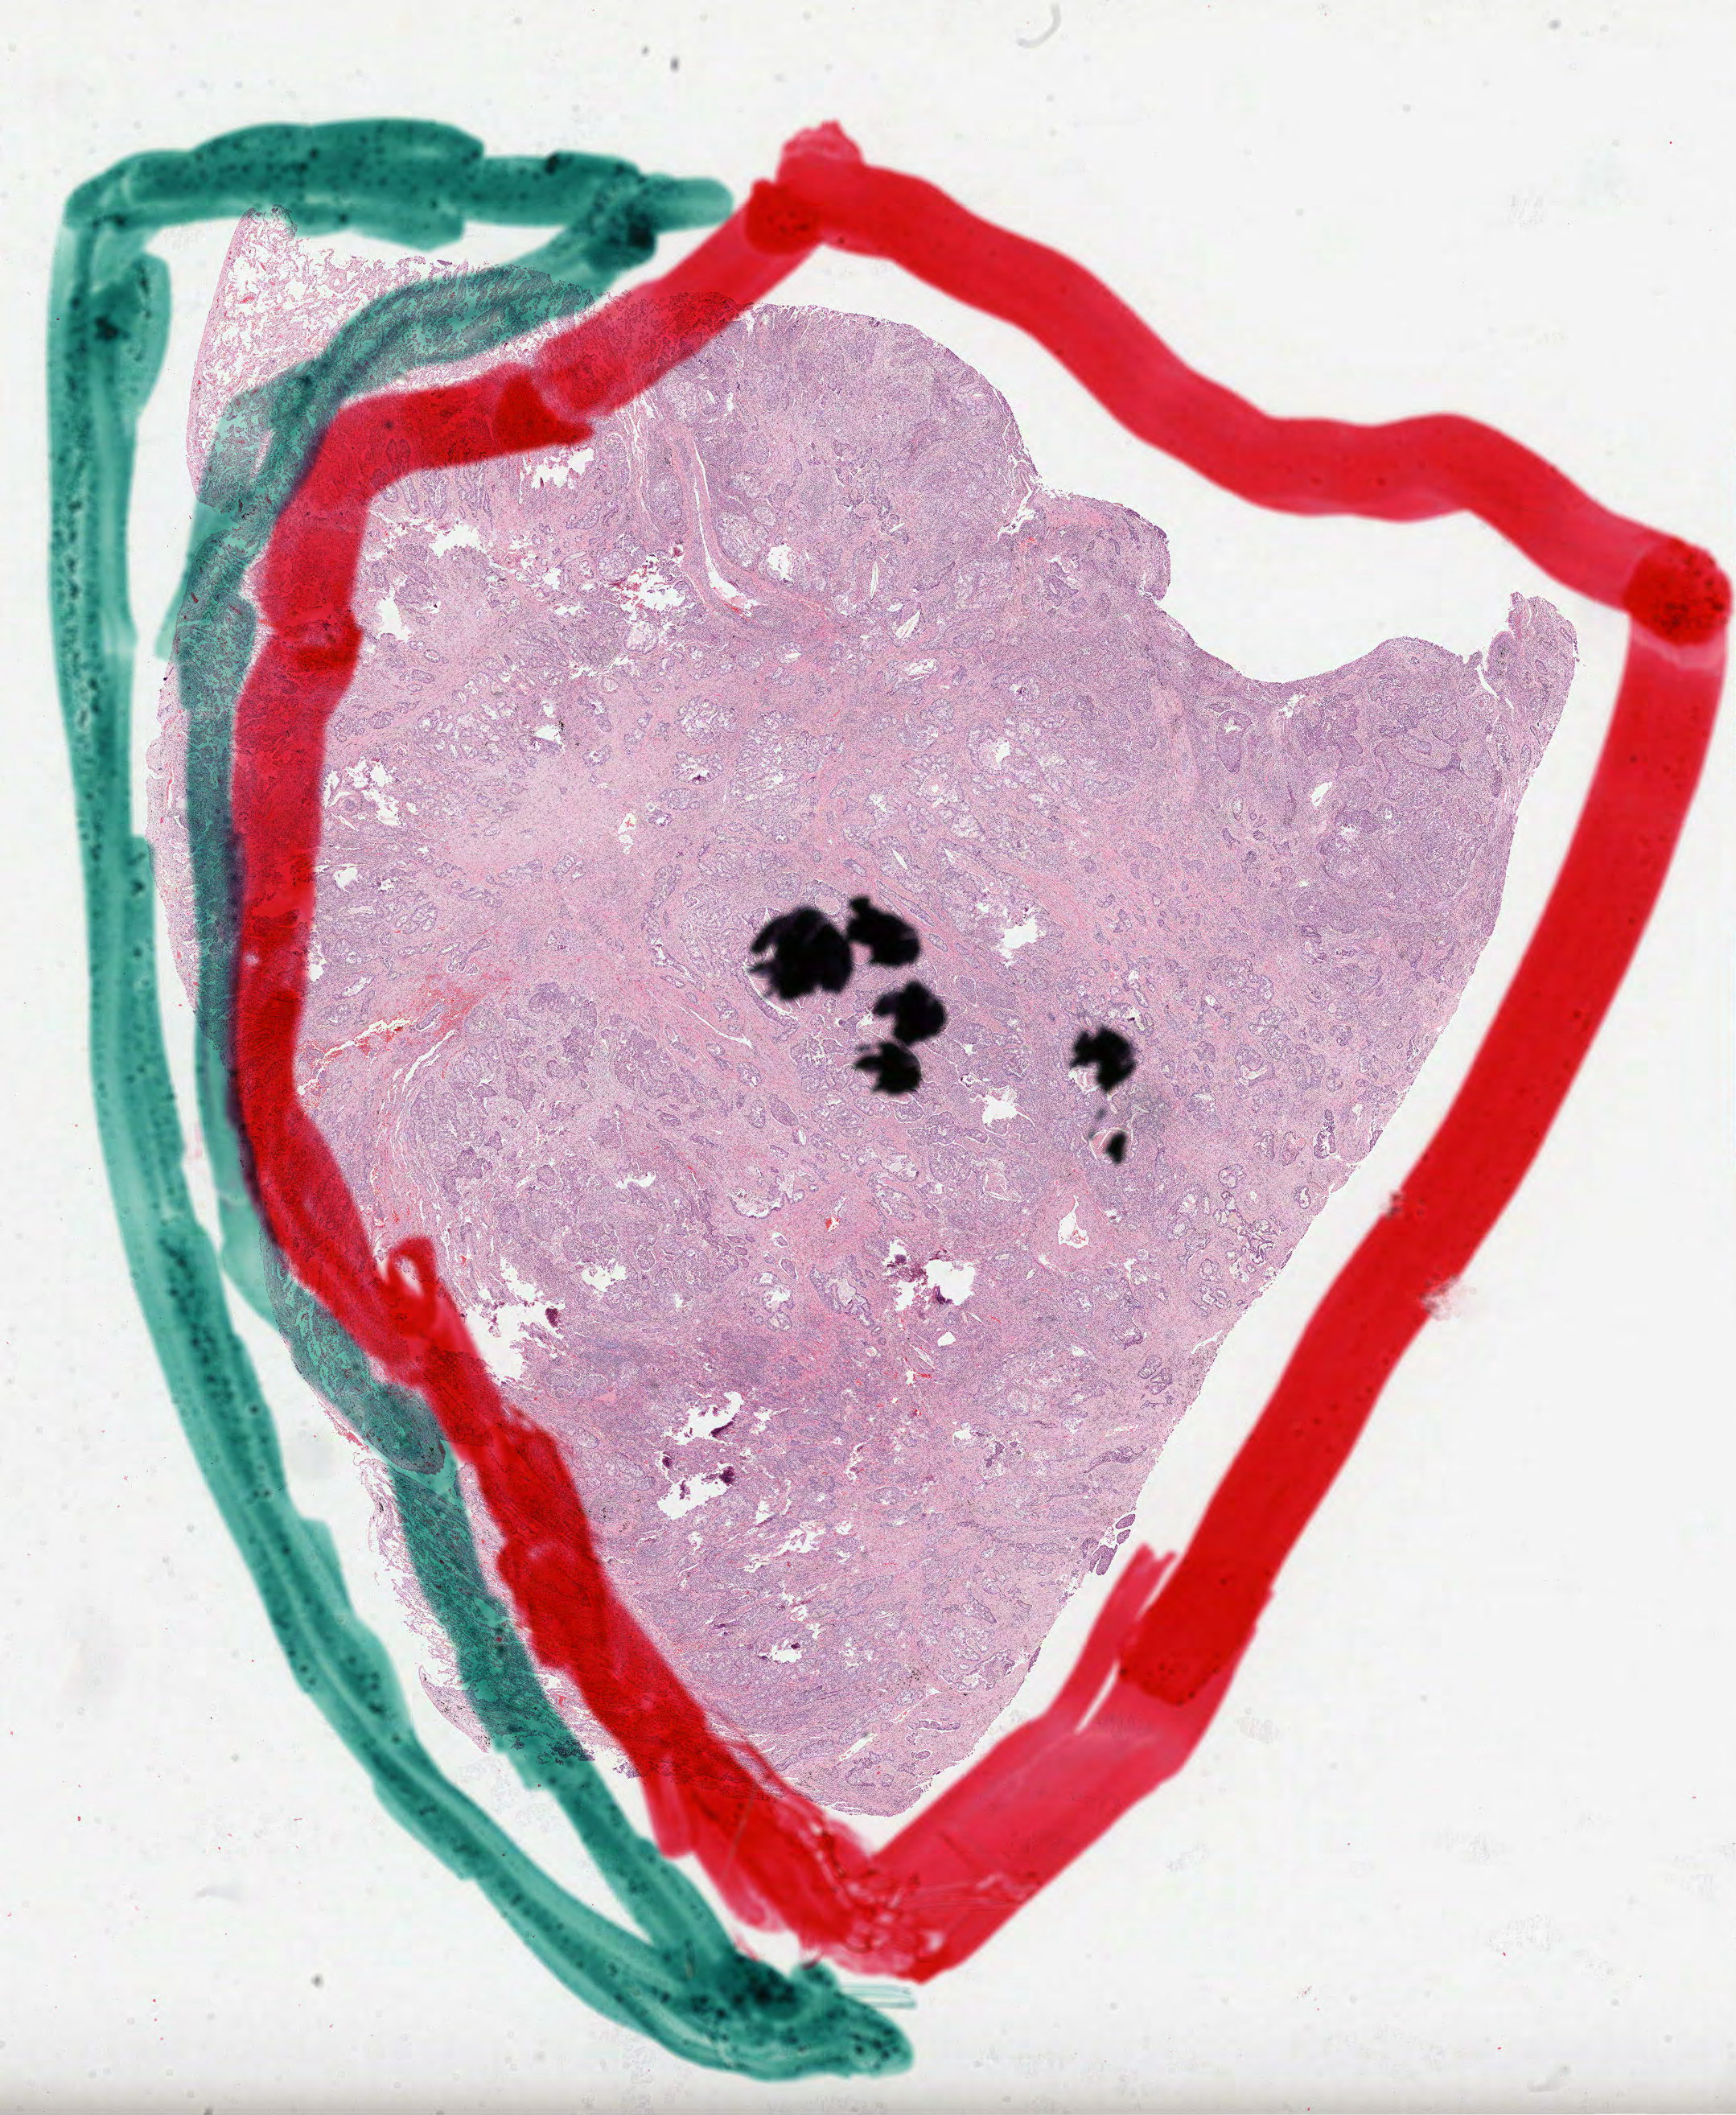
Whole-slide histology image, H&E, a low-resolution overview of the entire scanned area, about 17.4 x 21.2 mm; FFPE section; primary tumour sample from the lung. Male, age 66 years at initial diagnosis.
Laterality: right. AJCC pathologic stage: IV (7th edition). TNM: T2 N0 M1. Histologic diagnosis: Adenocarcinoma, NOS.